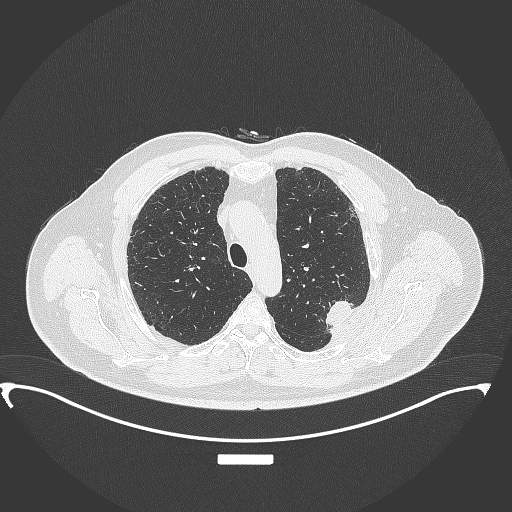
Chest CT, one axial slice. Position 273 of 350 along the scan axis. Reconstruction kernel B70f. Lung window (W 1500 / L -600 HU). 1 mm slice thickness. 512 × 512 image matrix, field of view 459 × 459 mm. Male patient, age 64 years. Case-level facts recorded for this patient, not image findings: clinical TNM (as recorded): T1c N1 M1.
Outlined on this slice (bounding box drawn by a radiologist):
- lung tumour (recorded histology: adenocarcinoma): bounding box <323,293,354,331> (left, top, right, bottom; pixels)